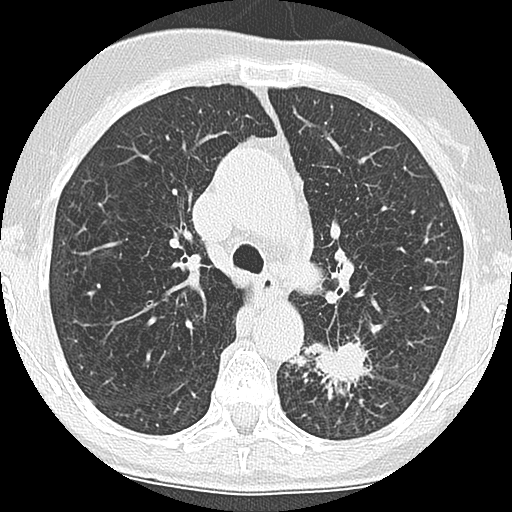
Low-dose screening chest CT, one axial slice; slice 119 of 171 in the series (ordered by position); reconstruction kernel LUNG; 120 kVp; lung window (W 1500 / L -600 HU); 512 × 512 image matrix.
Outlined on this slice (manually delineated by an expert):
- lesion 1 (tumor, lower lobe of left lung): bounding box (x1, y1, x2, y2) in pixels: (291, 342, 366, 388)